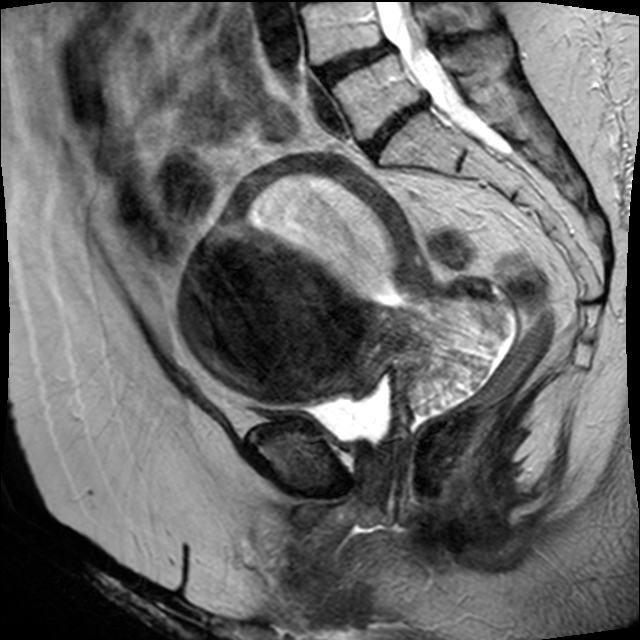
Pelvic MRI for cervical cancer, one sagittal slice. Position 23 of 45 along the scan axis. T2-weighted. 1.5 T. TE 89 ms, TR 4610 ms. 4 mm slice thickness. 640 × 640 image matrix, field of view 260 × 260 mm. Female patient, age 50 years.
Structures marked on this image (expert manual segmentation):
- uterus and cervix: bounding box (x1, y1, x2, y2) in pixels: (173, 150, 518, 420)